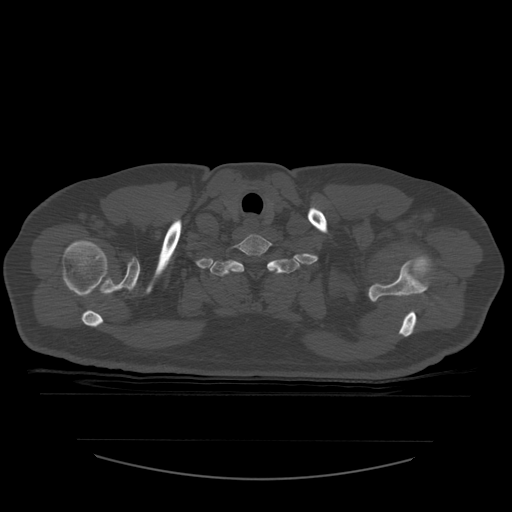
CT including the spine, one axial slice; position 474 of 532 along the scan axis; bone window (W 1800 / L 400 HU); 1.25 mm slice thickness; 512 × 512 image matrix. Patient age 44 years. Case-level facts recorded for this patient, not image findings: primary cancer: soft tissue sarcoma.
Outlined on this slice (semi-automatic segmentation, software-assisted and operator-edited):
- T1 vertebra: bounding box <210,246,300,277> (left, top, right, bottom; pixels)